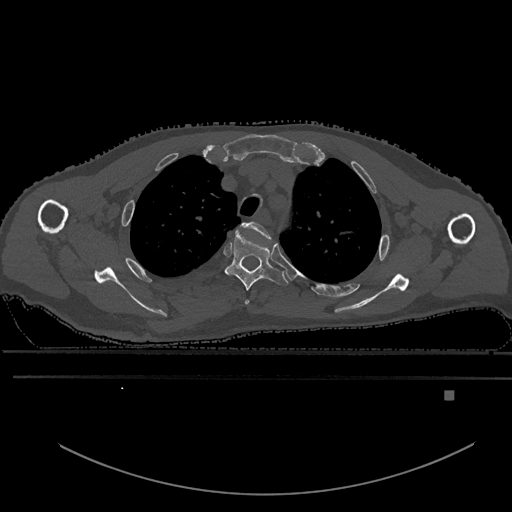
CT including the spine, one axial slice. Slice 457 of 969 in the series (ordered by position). Bone window (W 1800 / L 400 HU). 0.5 mm slice thickness. 512 × 512 image matrix, field of view 456 × 456 mm. Male patient, age 82 years. From the clinical record (not read from this slice): primary cancer: prostate; vertebrae with lytic lesions (as recorded): T11, T9, T8, T2.
Structures marked on this image (semi-automatic segmentation, software-assisted and operator-edited):
- T2 vertebra: bounding box <240,222,271,305> (left, top, right, bottom; pixels)
- T3 vertebra: <225,233,289,291>